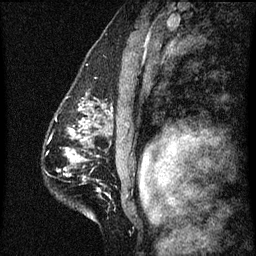
Breast MRI (dynamic contrast-enhanced), one sagittal slice; position 41 of 60 along the scan axis; dynamic contrast-enhanced series, image 2 of 3 at this slice position (ordered by acquisition); 1.5 T; TE 4.2 ms, TR 8 ms; 256 × 256 image matrix. Female patient, age 51 years.
Annotated regions visible in this slice (semi-automatically segmented with operator editing):
- analysis volume of interest (the breast-tissue region the enhancement analysis was run in; not a lesion): bounding box (x1, y1, x2, y2) in pixels: (66, 94, 102, 129)
- tumour enhancement mask (voxels above the 70 % enhancement threshold inside the analysis volume of interest): (80, 108, 82, 111)